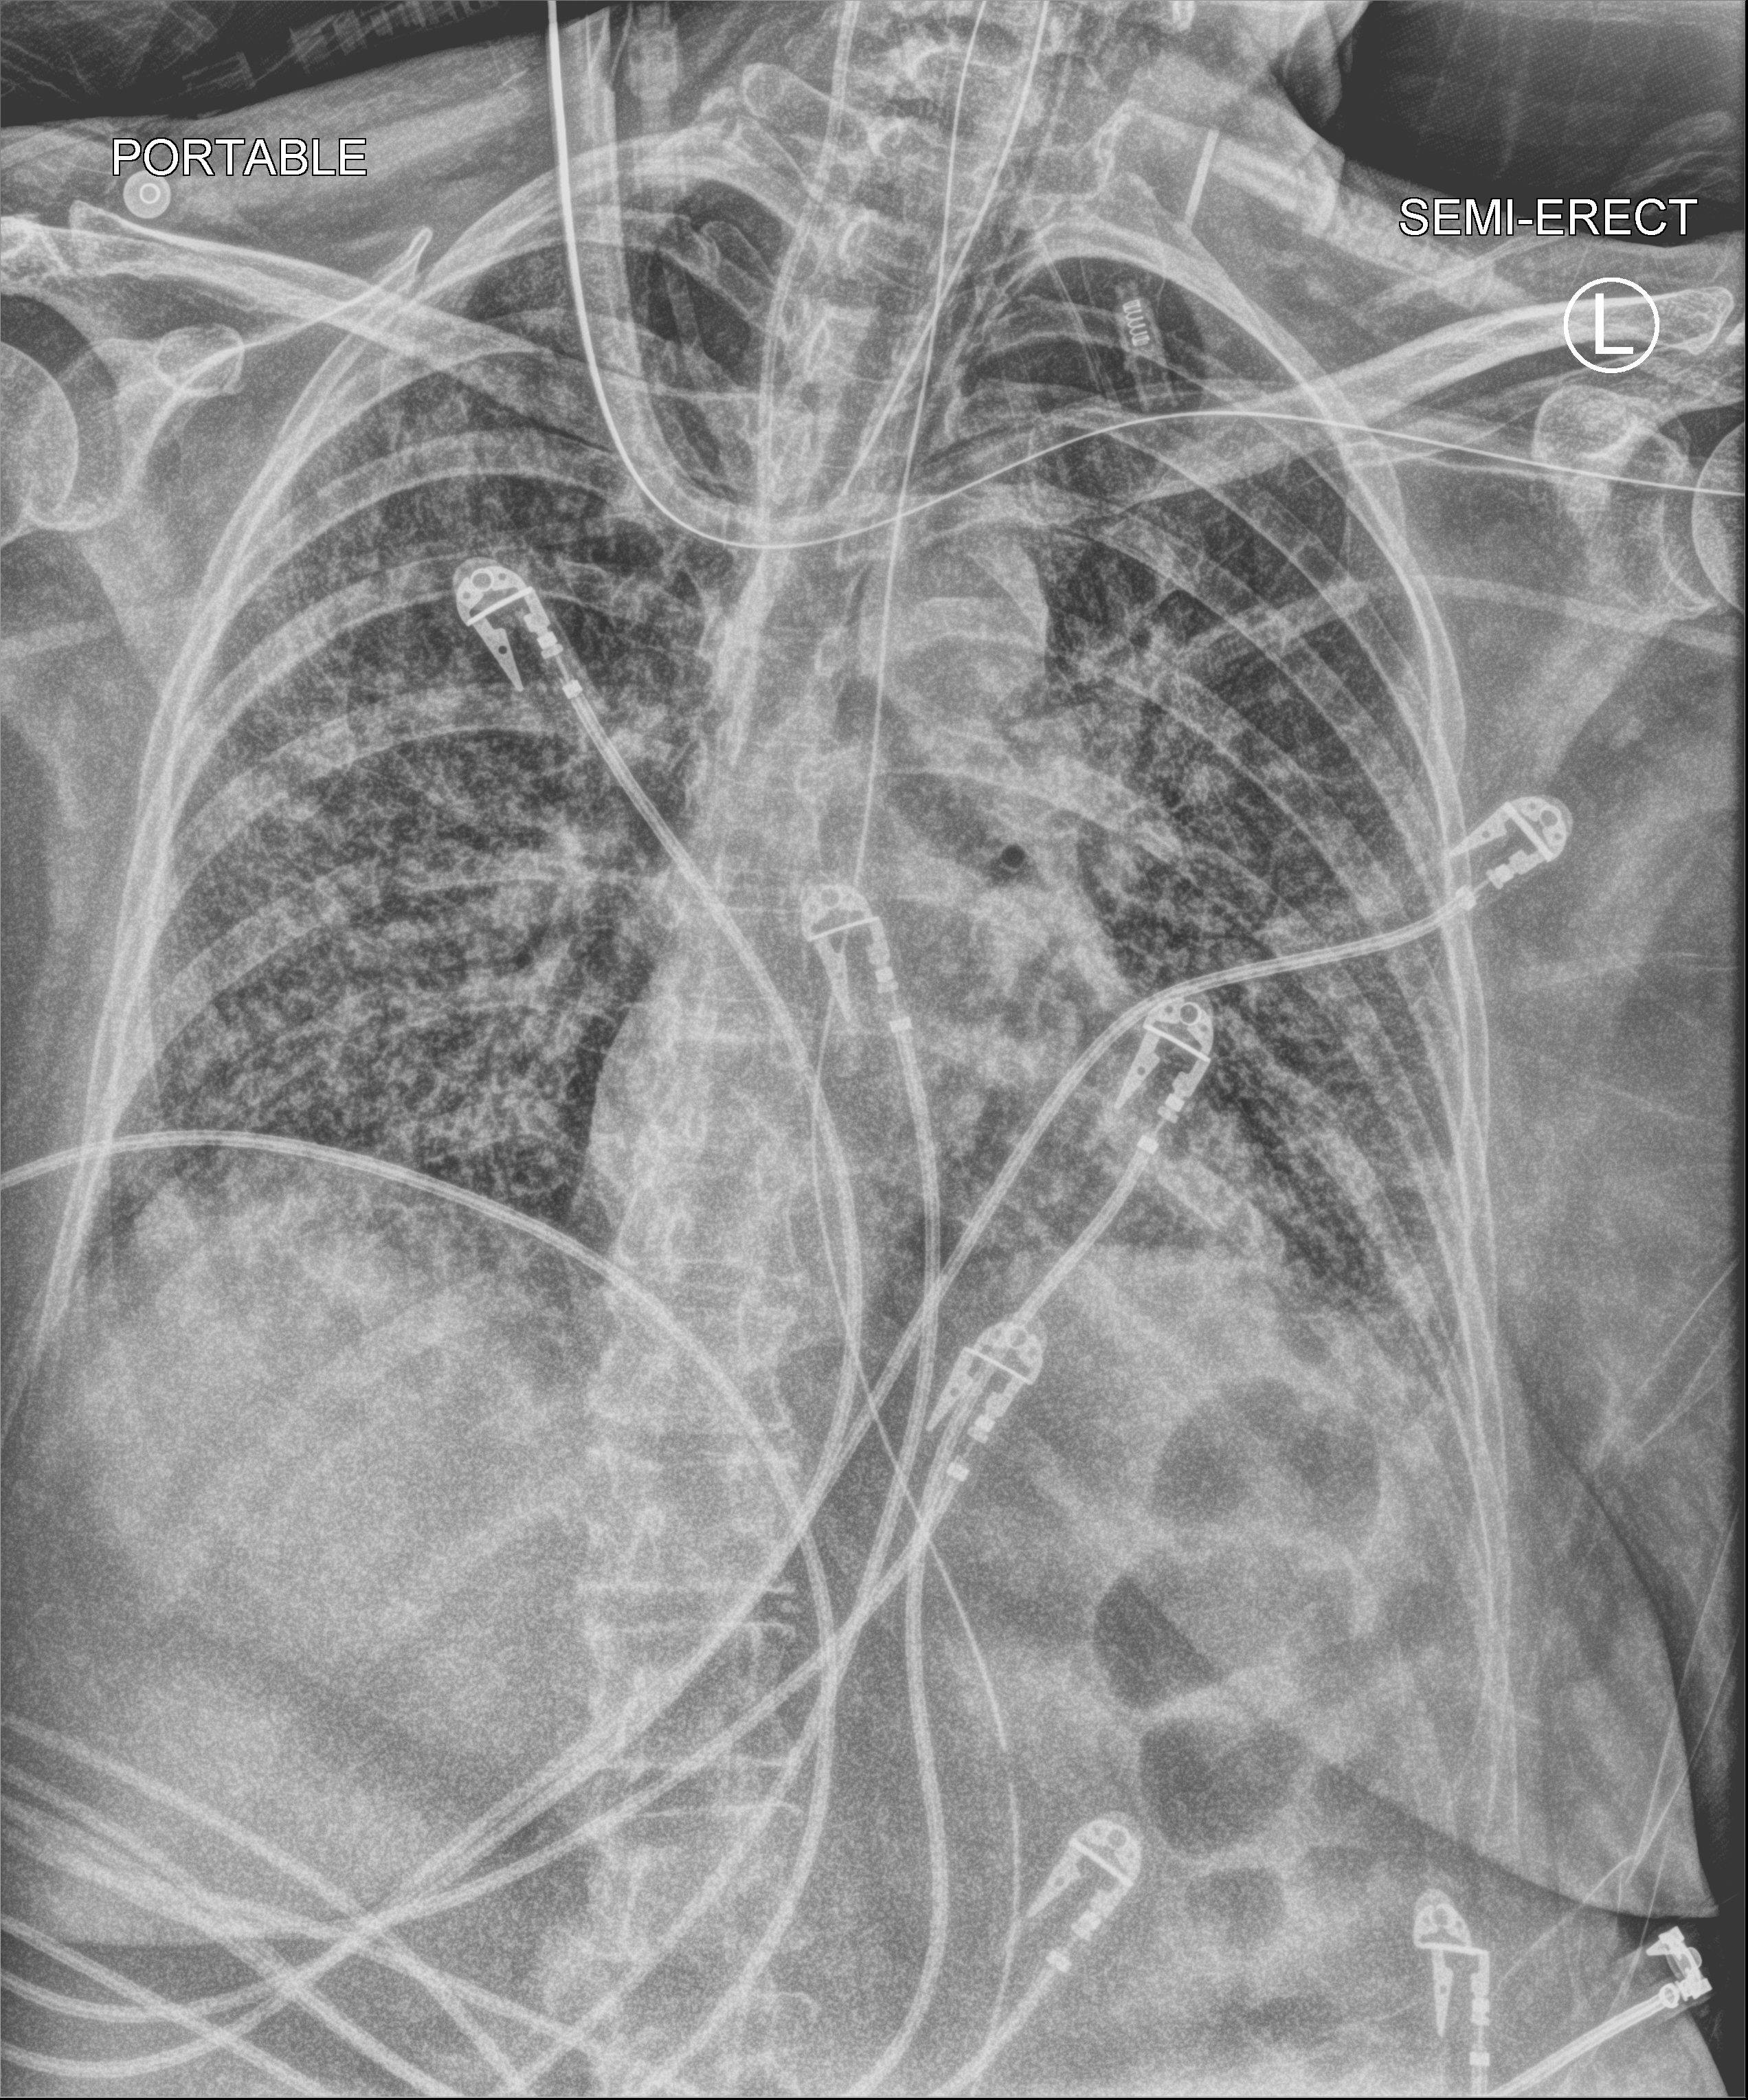
Bedside chest radiograph (computed radiography); anteroposterior (AP) projection. Female patient hospitalised with COVID-19, age 60–74 years.
From the hospital-stay record, not from the radiograph (when in the stay this image was taken is not recorded):
- length of hospital stay: 43 days
- diabetes (admission record): no
- mechanically ventilated during this hospital stay: yes